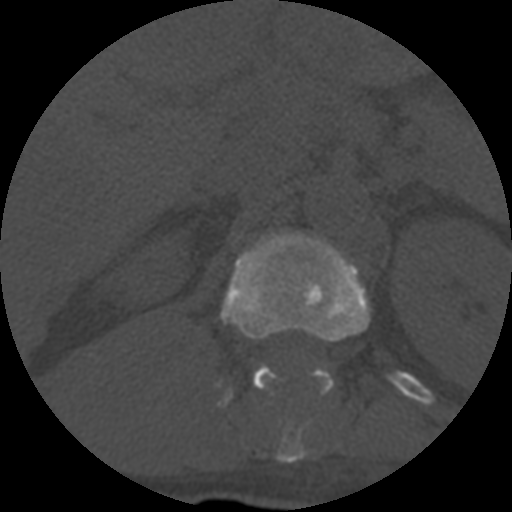
CT including the spine, one axial slice; position 306 of 708 along the scan axis; reconstruction kernel STANDARD; 120 kVp; one of 3 acquisitions stored at this slice position; bone window (W 1800 / L 400 HU); 512 × 512 image matrix, field of view 160 × 160 mm. Patient age 55 years. From the clinical record (not read from this slice): primary cancer: colon; vertebrae with lytic lesions (as recorded): T12, L1, L5.
Outlined on this slice (semi-automatically segmented with operator editing):
- T12 vertebra: bounding box (x1, y1, x2, y2) in pixels: (221, 232, 371, 463)